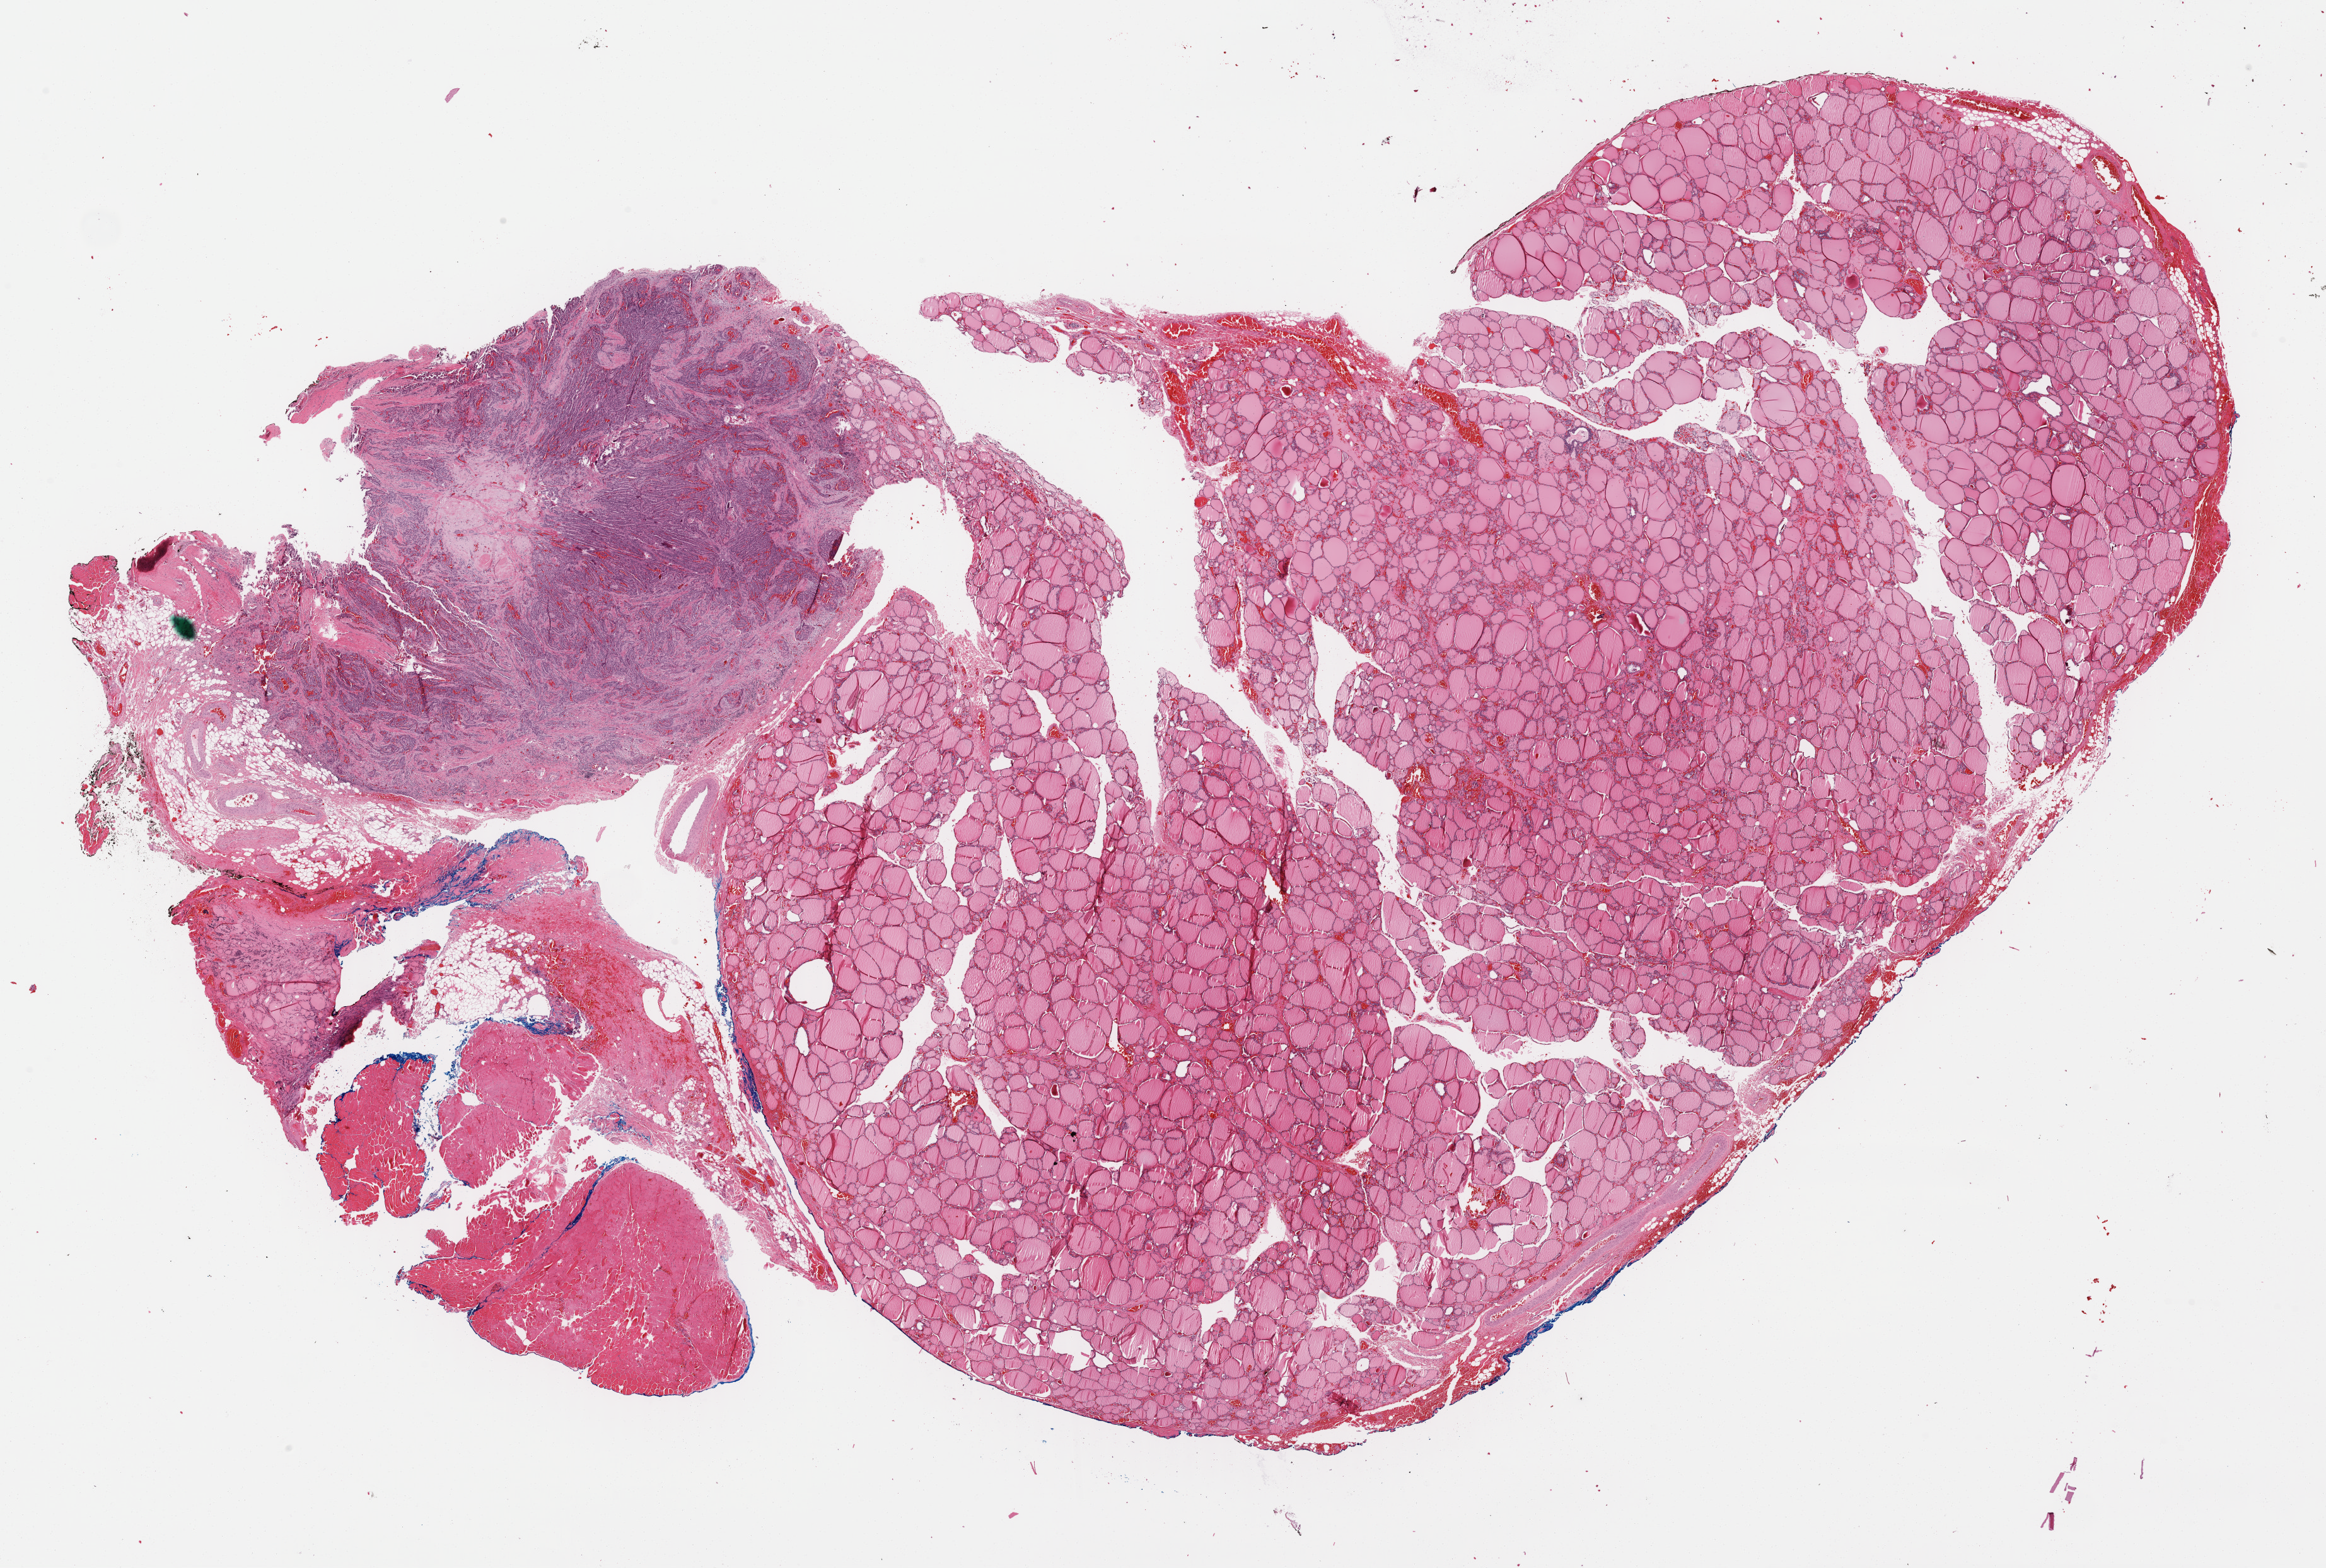
Digitized Hematoxylin and eosin (H&E) stained tissue section (whole slide), whole scanned area (about 29.1 x 19.6 mm, slide scanned at 40x) shown as a low-resolution overview; formalin-fixed paraffin-embedded (FFPE) diagnostic section; thyroid, primary tumour sample. Female patient; age at initial diagnosis 60 years.
AJCC pathologic stage: IVA (7th edition). TNM: T3 N1b M0. Lymph nodes positive (case pathology): 4 of 12 examined. Laterality: right. Histologic diagnosis: Papillary carcinoma, columnar cell (thyroid gland).